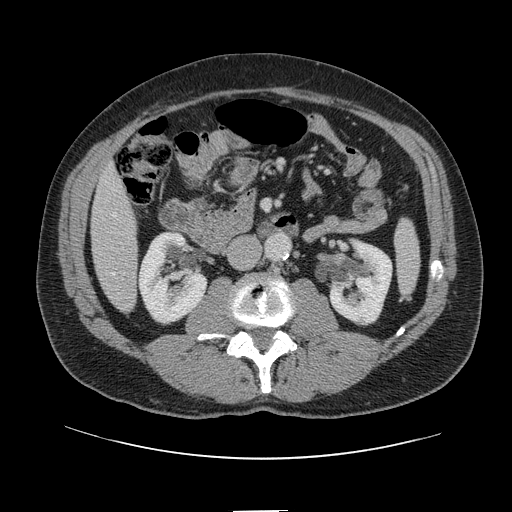
Contrast-enhanced abdominal CT, one axial slice. Position 26 of 161 along the scan axis. Intravenous contrast given. Soft-tissue window (W 400 / L 40 HU). 2.5 mm slice thickness. 512 × 512 image matrix, field of view 412 × 412 mm. Male patient, age 66 years. From the clinical record (not read from this slice): diagnosis: colorectal cancer liver metastases, imaged before liver resection; multiple liver metastases: no; largest metastasis: 3.5 cm; chemotherapy before resection: yes.
Outlined on this slice (outlined manually by an expert reader):
- hepatic veins: box from (x=112, y=214) to (x=116, y=275) px
- liver: (x=93, y=168)–(x=138, y=311)
- planned liver remnant (the part of the liver to remain after resection): (x=93, y=168)–(x=135, y=256)